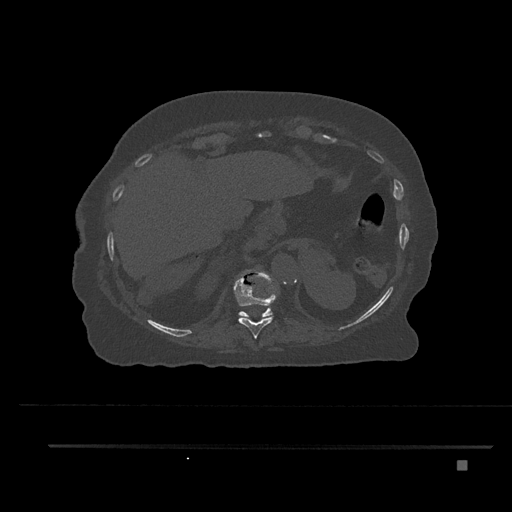
CT including the spine, one axial slice; slice 342 of 797 in the series (ordered by position); reconstruction kernel Br40s/3; 120 kVp; bone window (W 1800 / L 400 HU); 0.5 mm slice thickness; 512 × 512 image matrix. Female patient, age 76 years. From the clinical record (not read from this slice): primary cancer: lung; vertebrae with lytic lesions (as recorded): T11, L3.
Annotated regions visible in this slice (semi-automatic segmentation, software-assisted and operator-edited):
- T10 vertebra: bounding box [x1, y1, x2, y2] px = [234, 275, 276, 339]
- T11 vertebra: [238, 273, 276, 318]